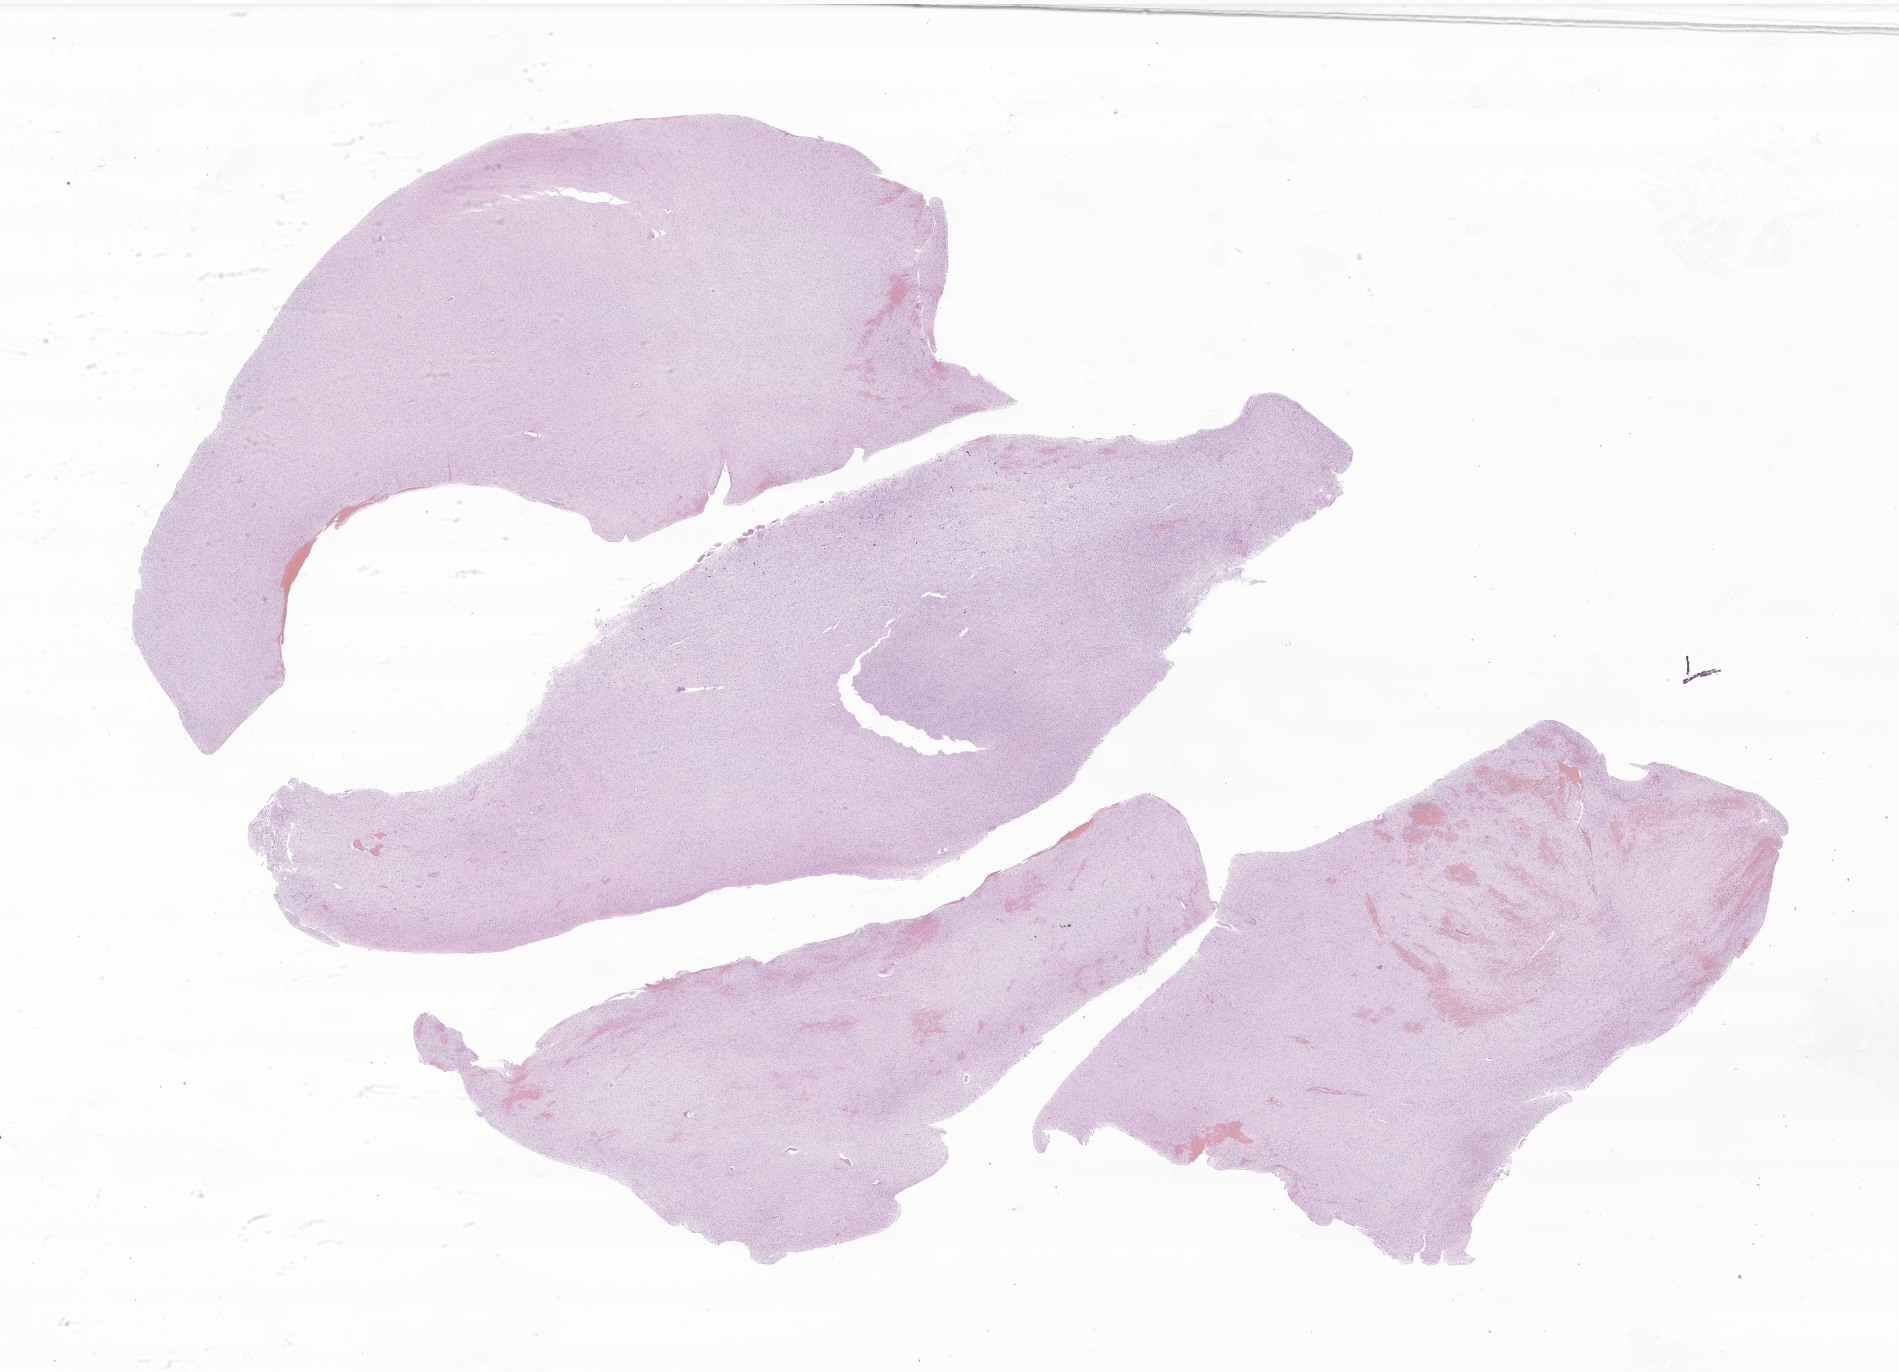
Whole-slide image, H&E stain of tumor tissue from the brain — whole scanned area (about 32.0 x 23.1 mm) shown as a low-resolution overview; FFPE section. Patient female; age 189 months (15 years 9 months).
Recorded diagnosis: Glioma, malignant.